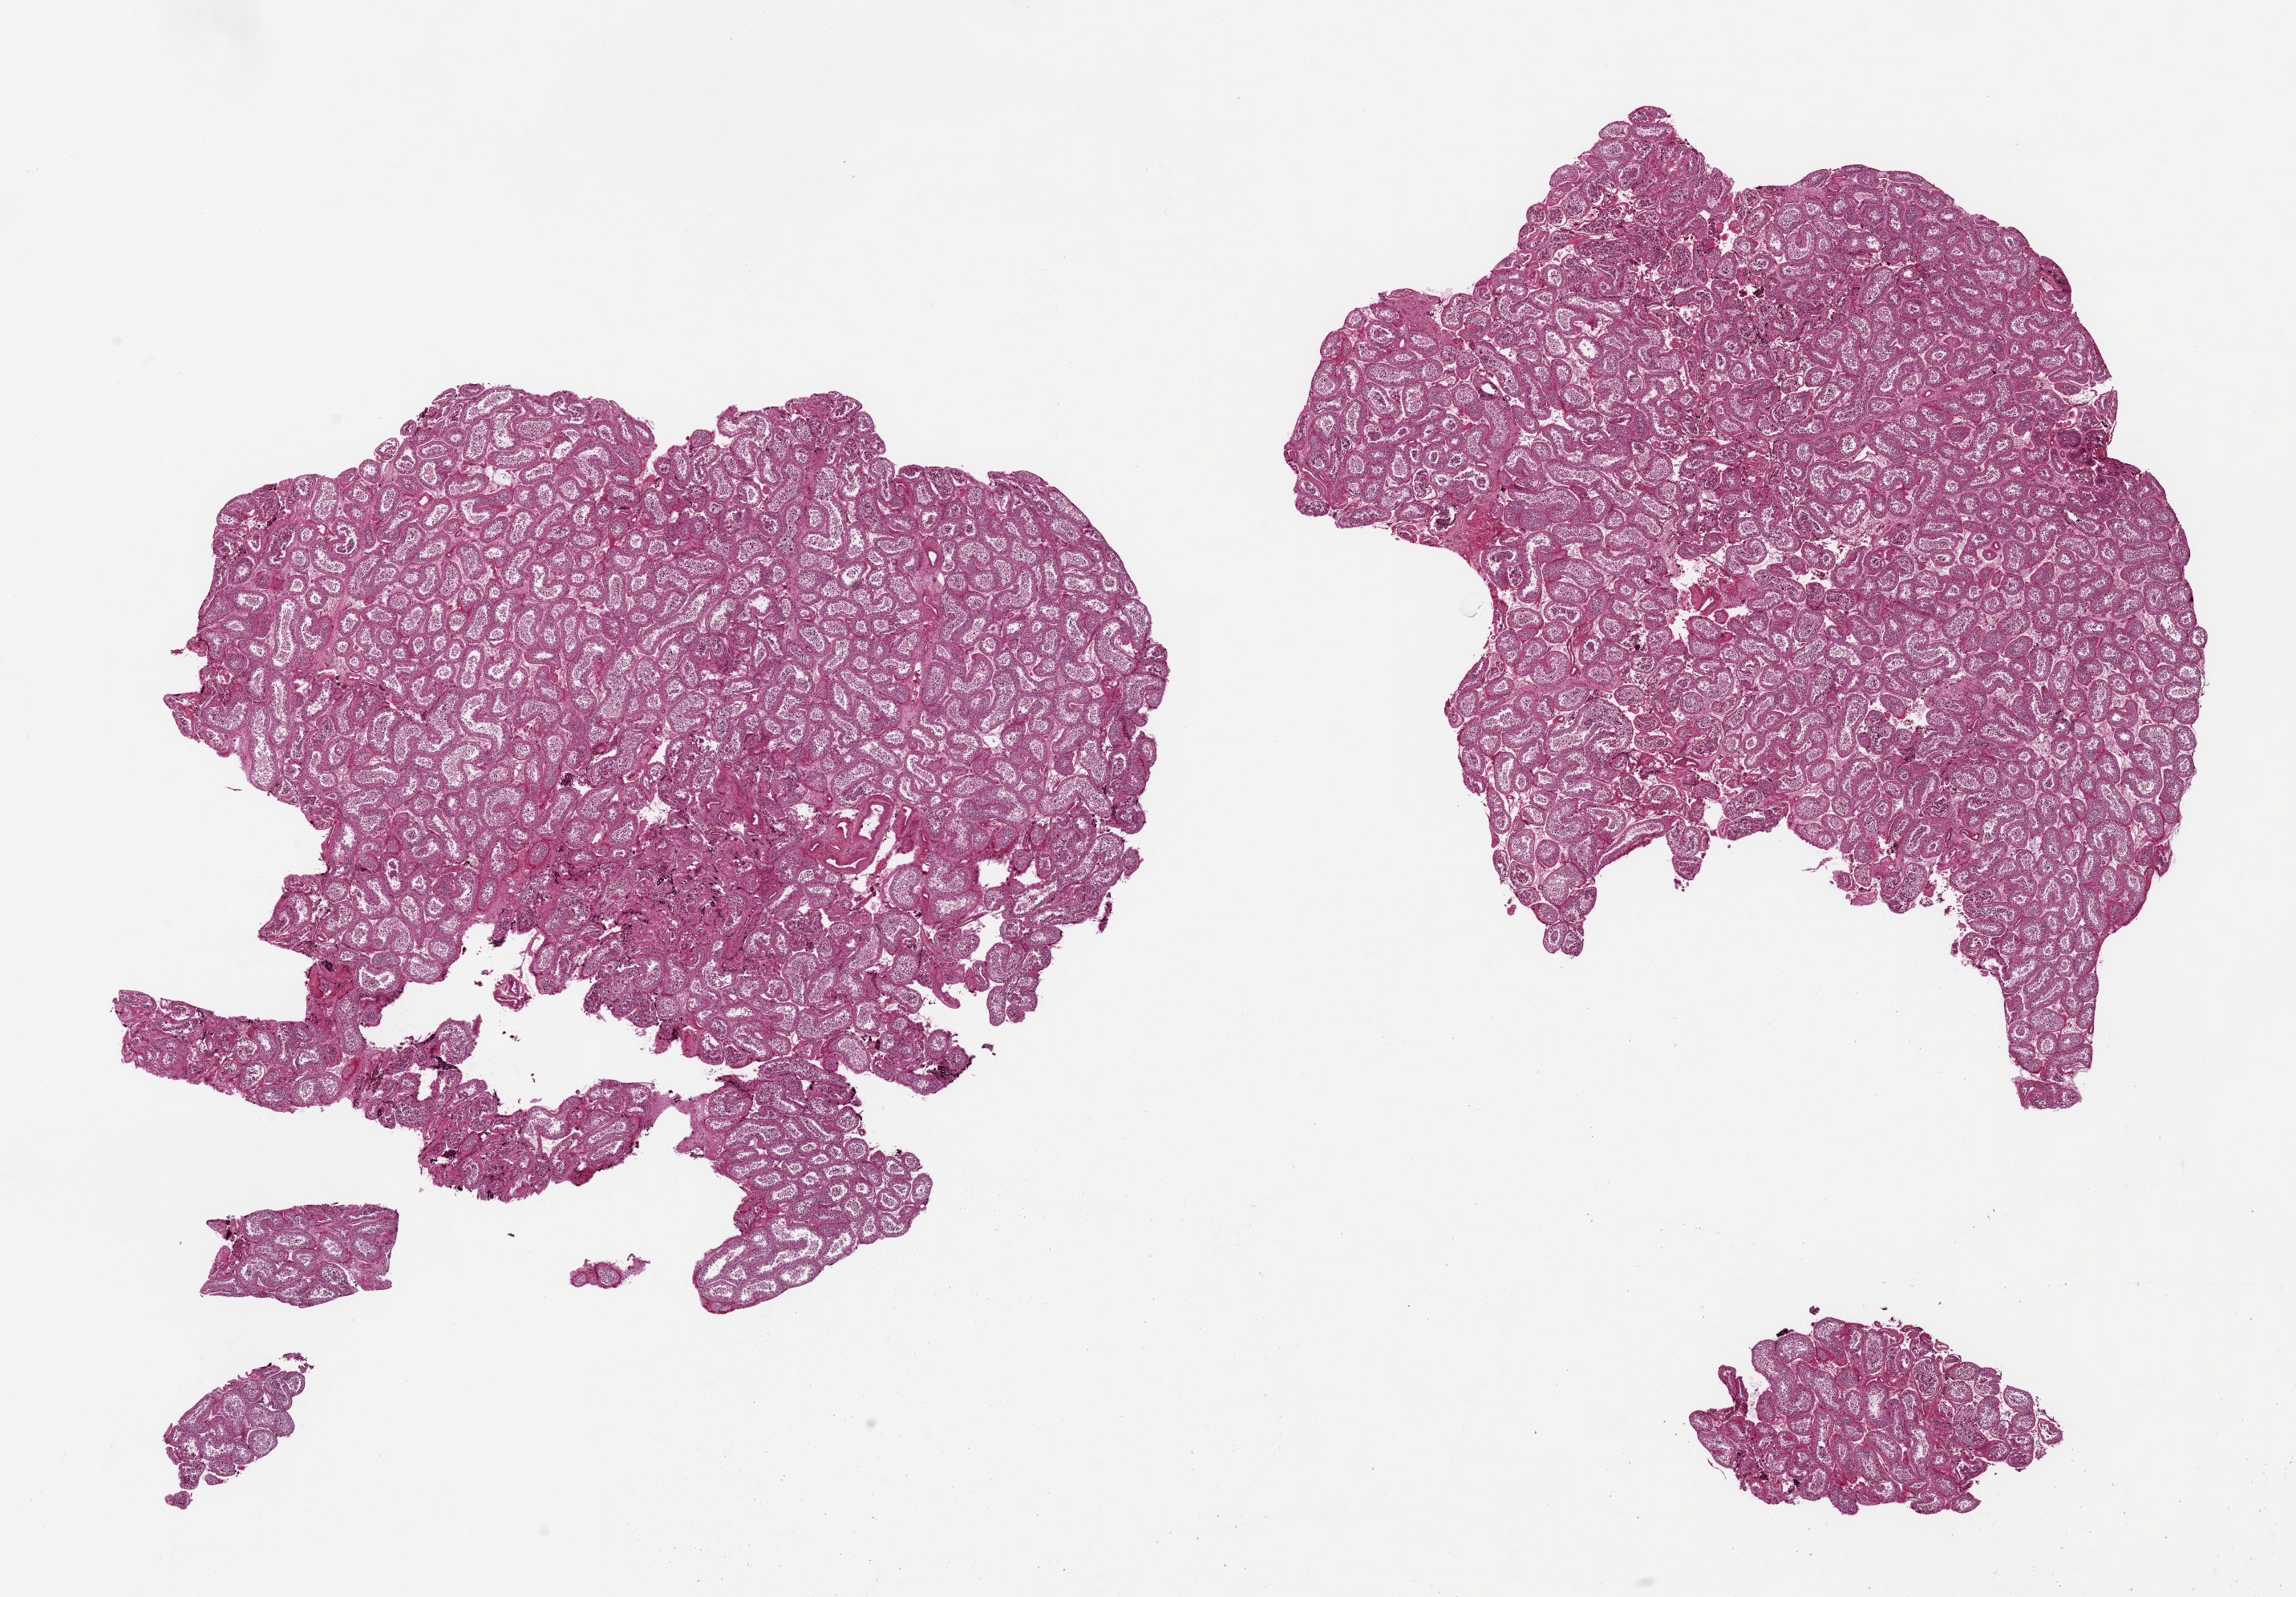
Haematoxylin and eosin whole-slide image, shown as a low-resolution overview of the whole scanned area (about 22.6 x 15.8 mm). PAXgene-fixed paraffin-embedded (PFPE) section. Sampled site (target tissue): testis. Tissue donor sample. Male donor.
Review note (as recorded): 2 pieces 10x8 & 9x9 mm; reduced spermatogenesis.